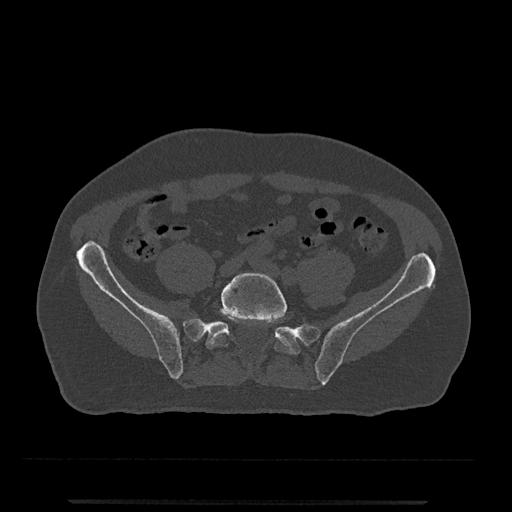
CT including the spine, one axial slice. Position 47 of 797 along the scan axis. Reconstruction kernel Br40s/3. 120 kVp. Bone window (W 1800 / L 400 HU). 0.5 mm slice thickness. 512 × 512 image matrix, field of view 419 × 419 mm. Male patient, age 63 years. From the clinical record (not read from this slice): primary cancer: prostate.
Annotated regions visible in this slice (semi-automatically segmented with operator editing):
- L5 vertebra: bounding box (x1, y1, x2, y2) in pixels: (209, 273, 292, 354)